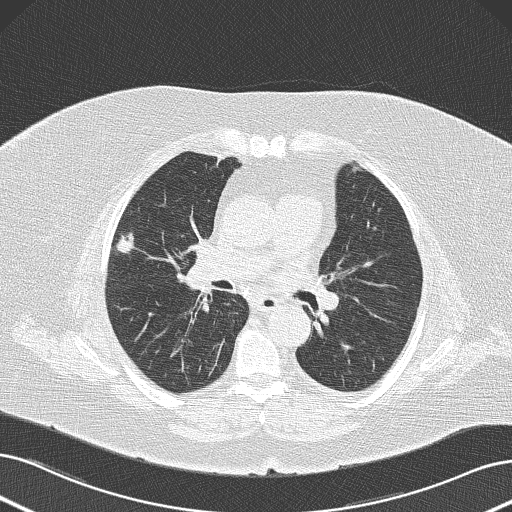
Axial slice from a low-dose chest CT screening exam. Baseline annual screen. Lung window (W 1500 / L -600 HU). 2 mm slice thickness. 120 kVp. Female, age 73 years at enrolment. Former smoker at enrolment.
• Expert-annotated lung lesion, bounding box [x1, y1, x2, y2] px = [101, 219, 147, 262].
• Screening reader's record for this exam (one nodule recorded; not confirmed to be the boxed lesion): non-calcified nodule or mass ≥4 mm, right upper lobe, 15 × 11 mm, poorly defined margins, soft tissue attenuation.
• Participant outcome: lung cancer diagnosed 55 days after this screen — neoplasm, malignant, right upper lobe, stage IA (AJCC 6th edition), 15 mm at pathology.